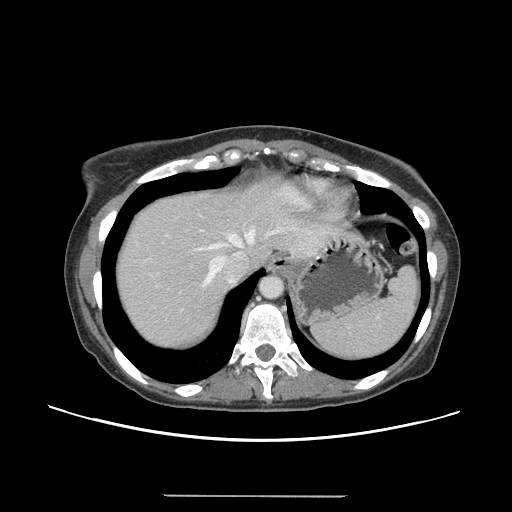
Contrast-enhanced abdominal CT, one axial slice; slice 122 of 144 in the series (ordered by position); intravenous contrast given; soft-tissue window (W 400 / L 40 HU); 512 × 512 image matrix, field of view 380 × 380 mm. Female patient, age 53 years. Case-level facts recorded for this patient, not image findings: diagnosis: colorectal cancer liver metastases, imaged before liver resection; multiple liver metastases: yes; largest metastasis: 1.1 cm.
Outlined on this slice (outlined manually by an expert reader):
- hepatic veins: box from (x=197, y=229) to (x=278, y=286) px
- liver: (x=116, y=179)–(x=325, y=348)
- planned liver remnant (the part of the liver to remain after resection): (x=116, y=178)–(x=276, y=296)